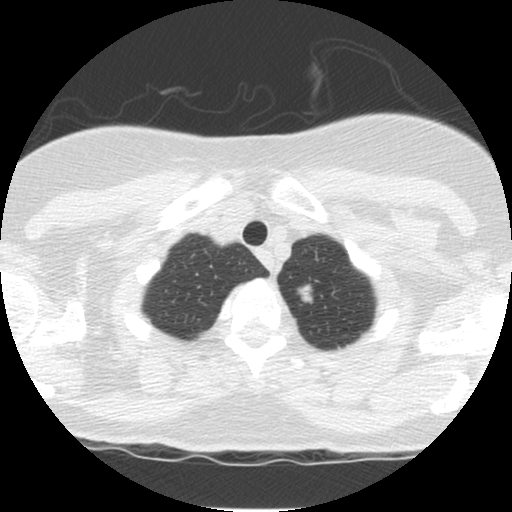
Low-dose screening chest CT, one axial slice; position 111 of 120 along the scan axis; reconstruction kernel STANDARD; 120 kVp; lung window (W 1500 / L -600 HU); 2.5 mm slice thickness; 512 × 512 image matrix, field of view 300 × 300 mm.
Outlined on this slice (outlined manually by an expert reader):
- lesion 1 (tumor, upper lobe of left lung): bounding box [x1, y1, x2, y2] px = [298, 283, 314, 304]